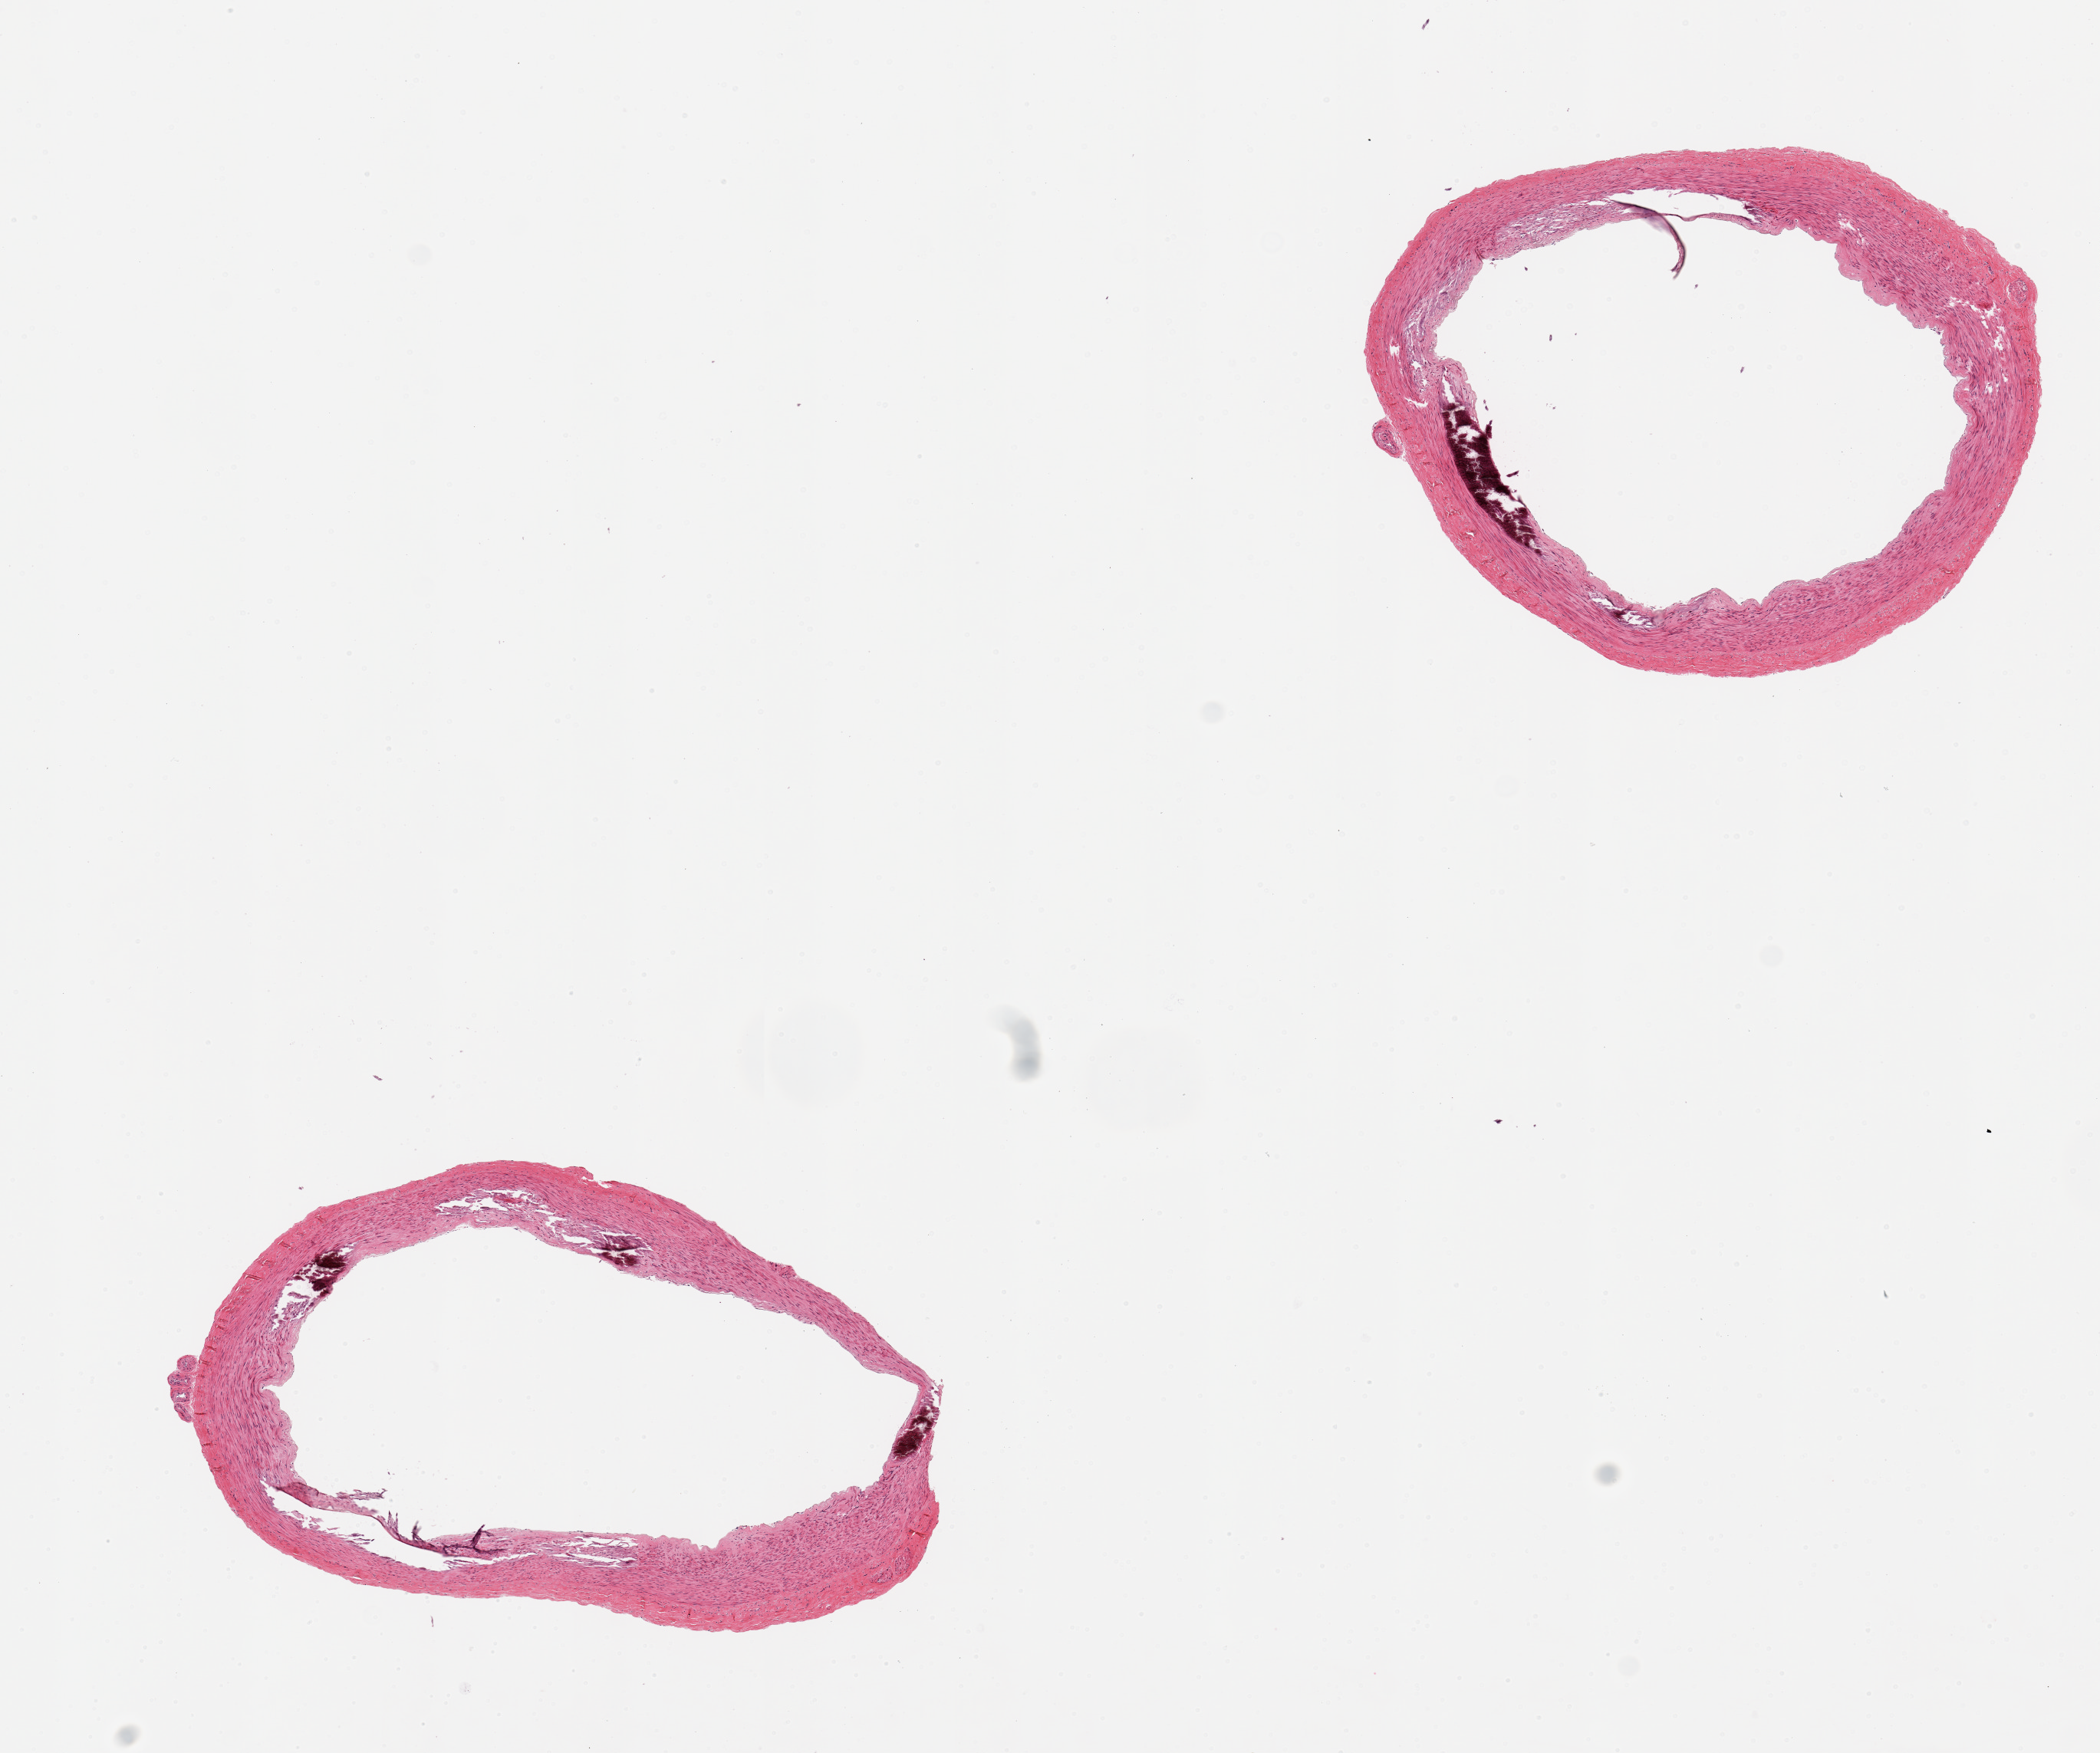
Digitized hematoxylin and eosin (H&E)-stained section, brightfield — a low-resolution overview of the entire scanned area, about 10.8 x 9.0 mm, PAXgene-fixed paraffin-embedded (PFPE) section, target tissue: tibial artery, tissue donor sample. Donor sex: male.
• pathologist's review note for this sample: 2 pieces, minimal-absent atherosis, Monckeberg's medial sclerosis